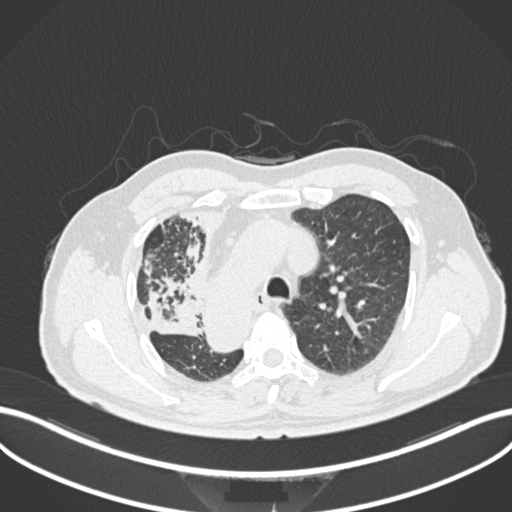
Chest CT, one axial slice; slice 172 of 206 in the series (ordered by position); reconstruction kernel B30f; 120 kVp; lung window (W 1500 / L -600 HU); 1 mm slice thickness; 512 × 512 image matrix. Patient: male, 67 years. From the clinical record (not read from this slice): clinical TNM (as recorded): T2a N0 M0.
Outlined on this slice (bounding box drawn by a radiologist):
- lung tumour (recorded histology: squamous cell carcinoma): box from (x=141, y=284) to (x=203, y=338) px